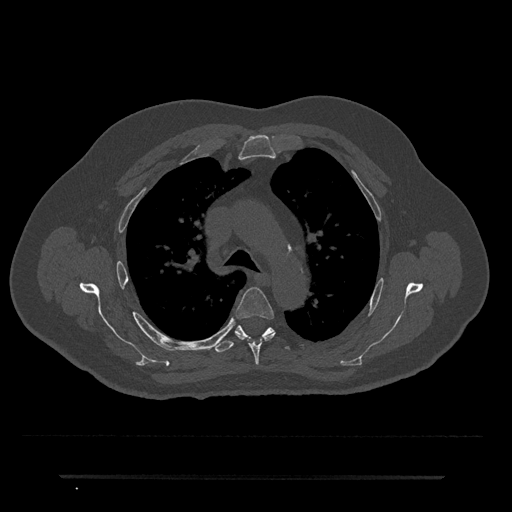
CT including the spine, one axial slice. Slice 511 of 797 in the series (ordered by position). 120 kVp. Bone window (W 1800 / L 400 HU). 0.5 mm slice thickness. 512 × 512 image matrix, field of view 437 × 437 mm. Patient: male, 69 years. From the clinical record (not read from this slice): primary cancer: prostate.
Outlined on this slice (semi-automatic segmentation, software-assisted and operator-edited):
- T4 vertebra: bounding box (x1, y1, x2, y2) in pixels: (234, 287, 275, 365)
- T5 vertebra: (213, 325, 290, 353)